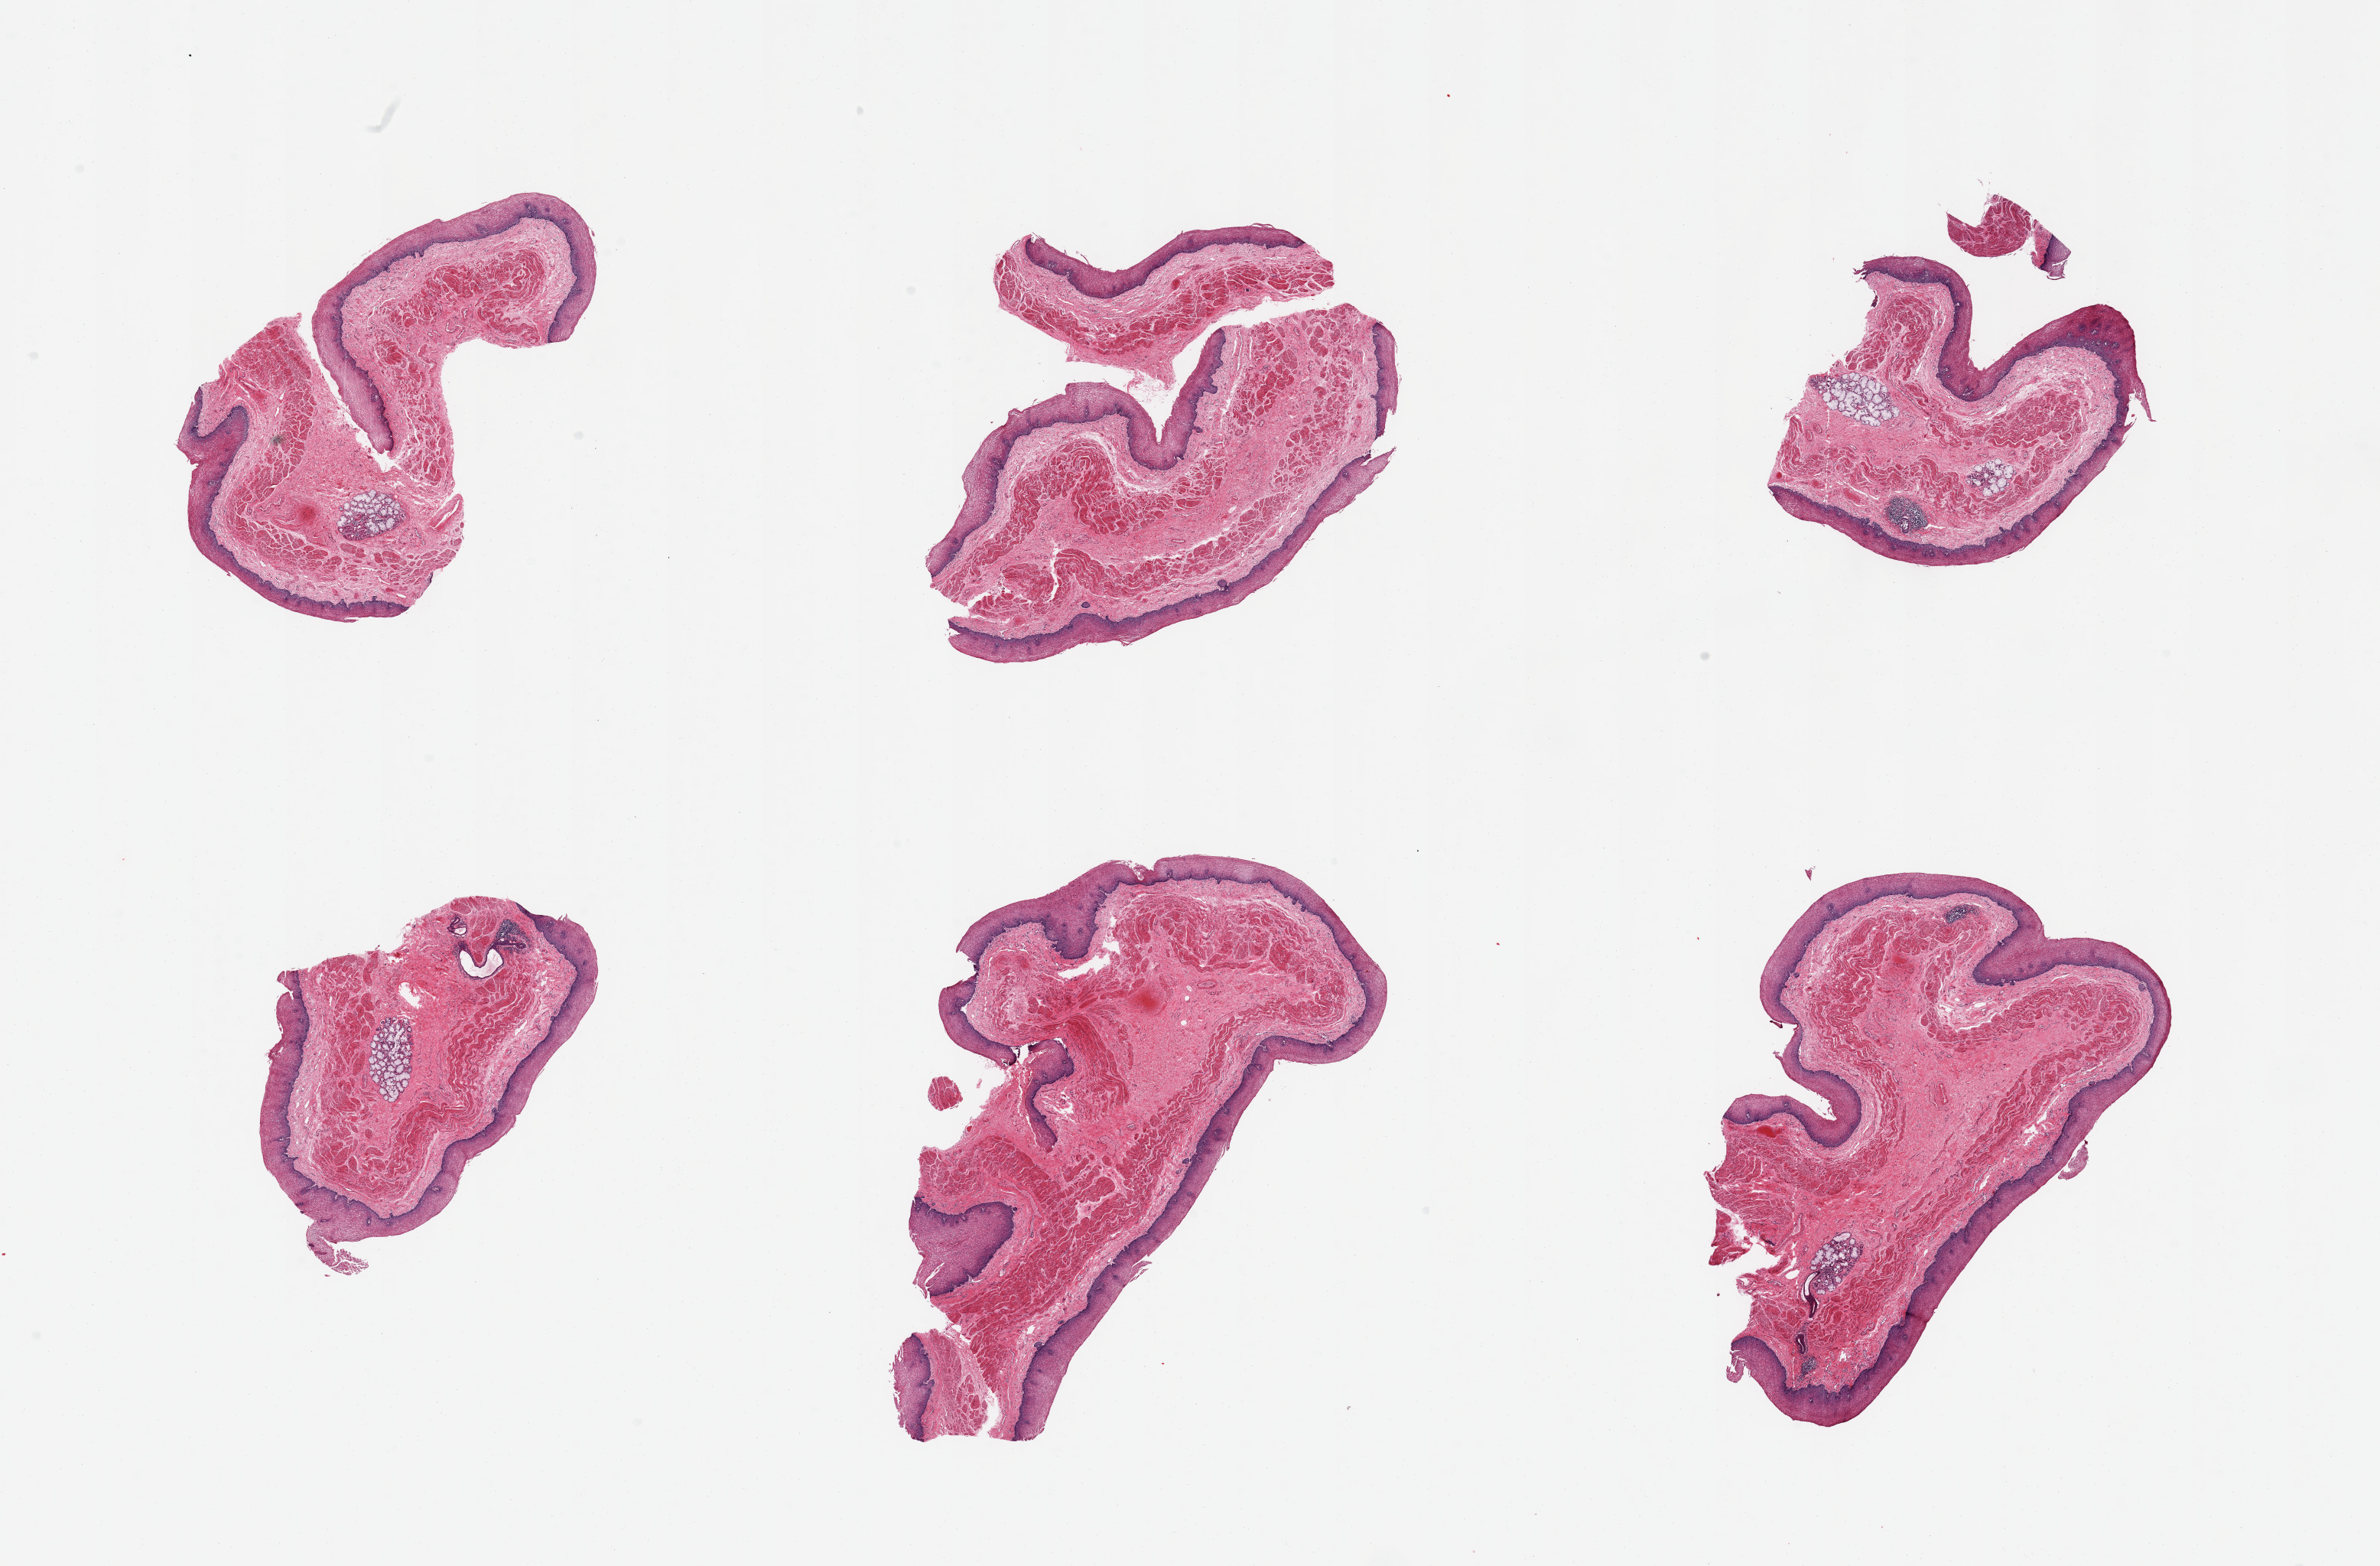
Whole-slide image, H&E stain, shown as a low-resolution overview of the whole scanned area (about 24.6 x 16.2 mm). PAXgene-fixed, paraffin-embedded tissue. Target tissue: esophageal mucous membrane. Donor tissue sample.
Pathologist's review note for this sample: 6 pieces, squamous mucosa up to ~0.2mm, ~10% thicknesss--few submucosal mucus glands noted.